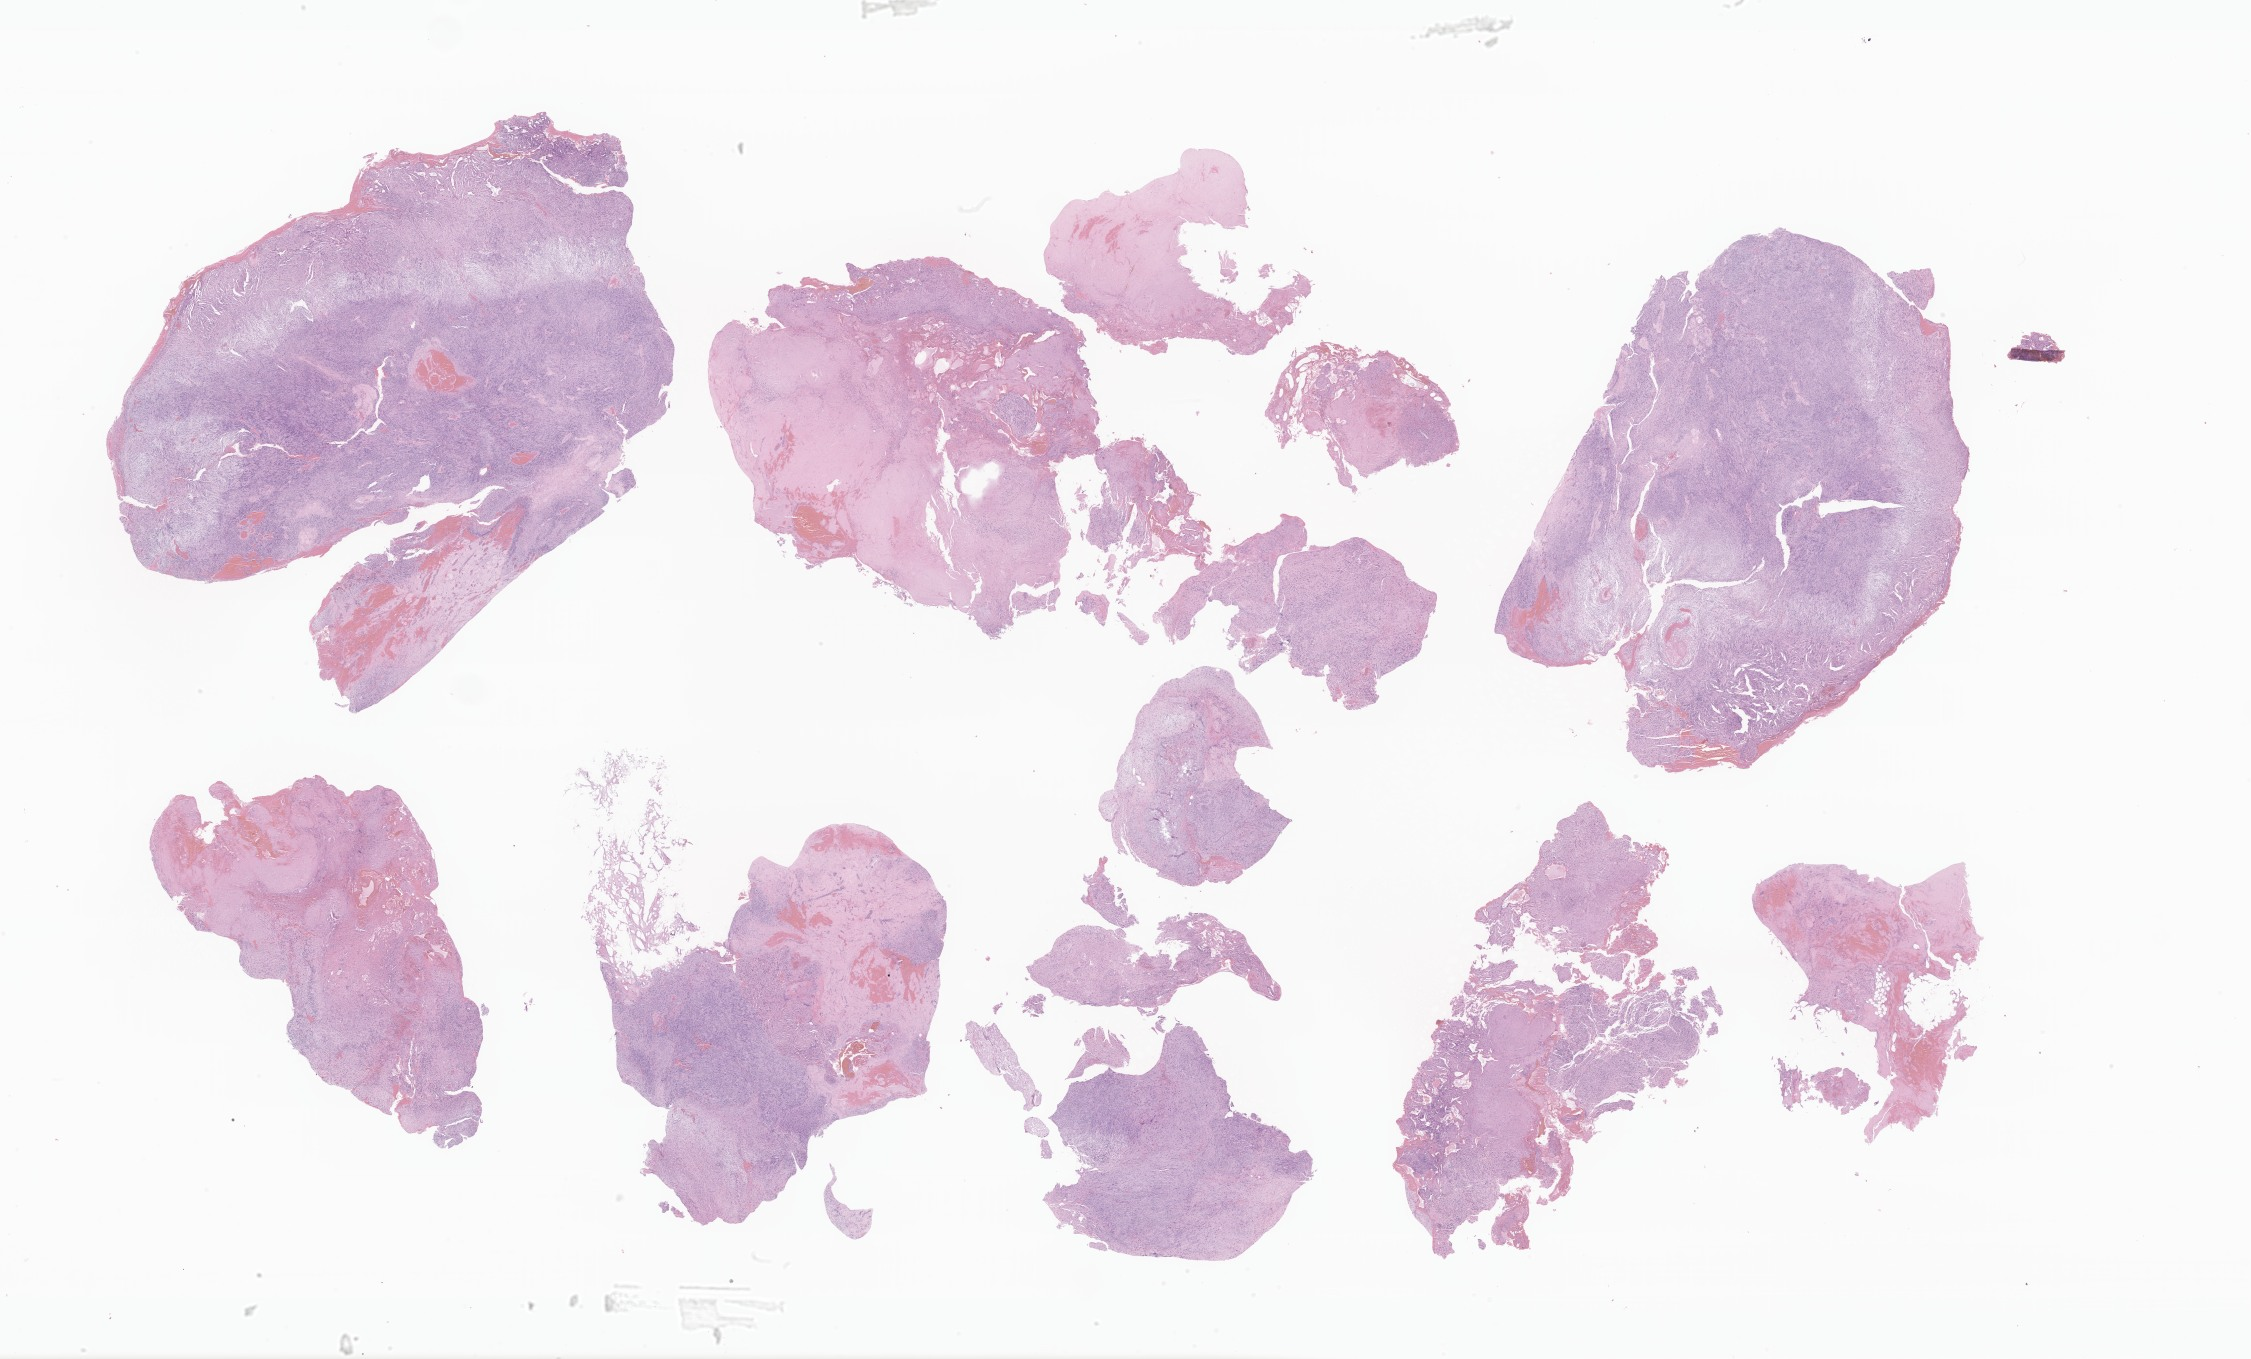
Digitized H&E-stained section of tumor tissue from the brain — low-resolution overview of the scanned area, about 38.0 x 22.9 mm, FFPE section. Female patient, age 205 months (17 years 1 month).
Recorded diagnosis: Neurofibromatosis, NOS.